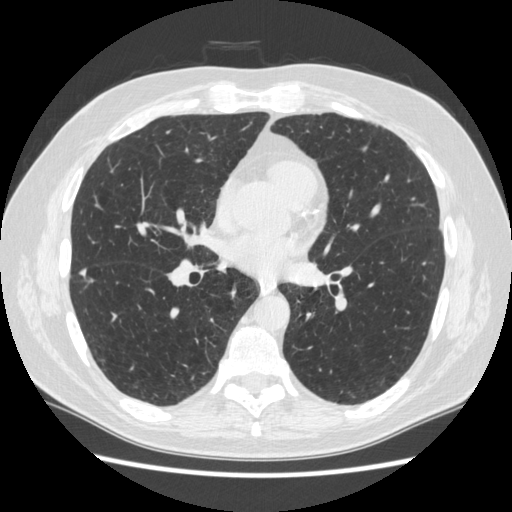
Low-dose screening chest CT, one axial slice. Position 128 of 267 along the scan axis. Reconstruction kernel STANDARD. Lung window (W 1500 / L -600 HU). 1.25 mm slice thickness. 512 × 512 image matrix, field of view 360 × 360 mm.
Outlined on this slice (expert manual segmentation):
- lesion 2 (nodule, lower lobe of right lung): bounding box [x1, y1, x2, y2] px = [80, 269, 86, 276]